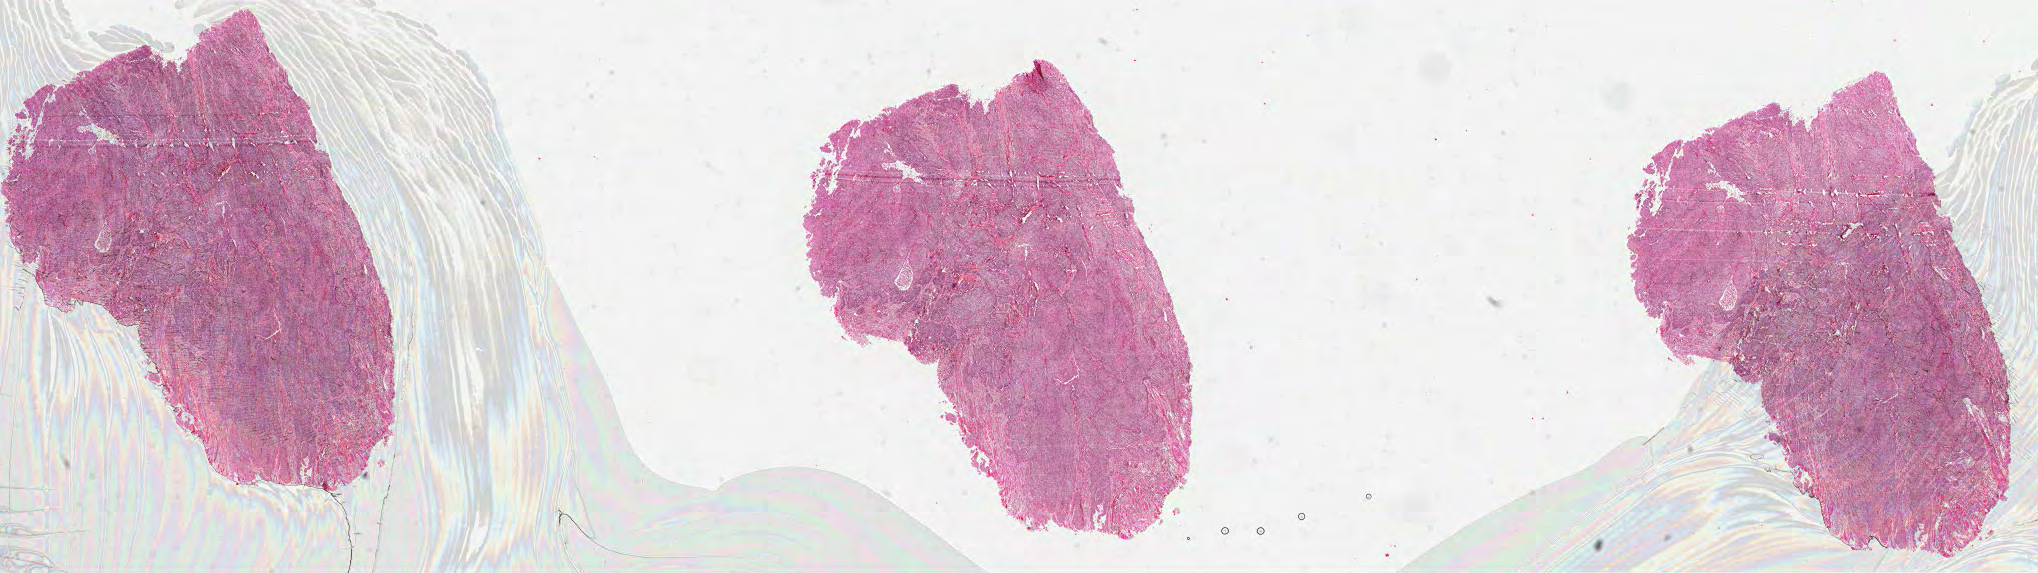
Whole-slide histology image, H&E-stained — whole scanned area (about 32.9 x 9.2 mm) shown as a low-resolution overview. Formalin-fixed paraffin-embedded (FFPE) diagnostic section. Primary tumour sample from the head and neck. Female, age 45 years at initial diagnosis. Histologic grade: G2 (moderately differentiated).
AJCC pathologic stage: IVA (6th edition). Pathologic diagnosis: Squamous cell carcinoma, NOS (tongue, NOS).